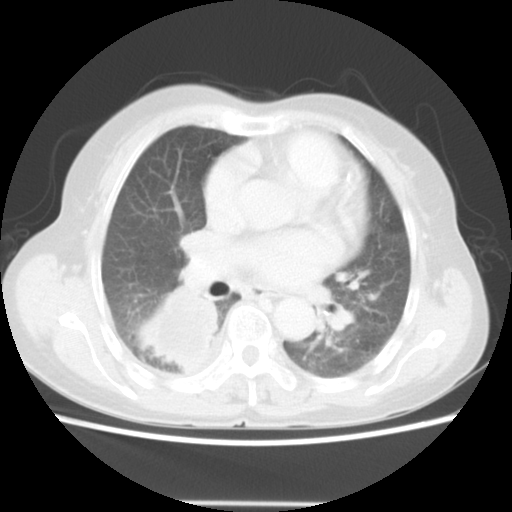
Chest CT, one axial slice. Slice 27 of 52 in the series (ordered by position). Lung window (W 1500 / L -600 HU). 5 mm slice thickness. 512 × 512 image matrix, field of view 337 × 337 mm. Patient: female, 67 years. From the clinical record (not read from this slice): clinical TNM (as recorded): T3 N1 M1.
Annotated regions visible in this slice (bounding box drawn by a radiologist):
- lung tumour (recorded histology: adenocarcinoma): bounding box (x1, y1, x2, y2) in pixels: (139, 289, 223, 377)